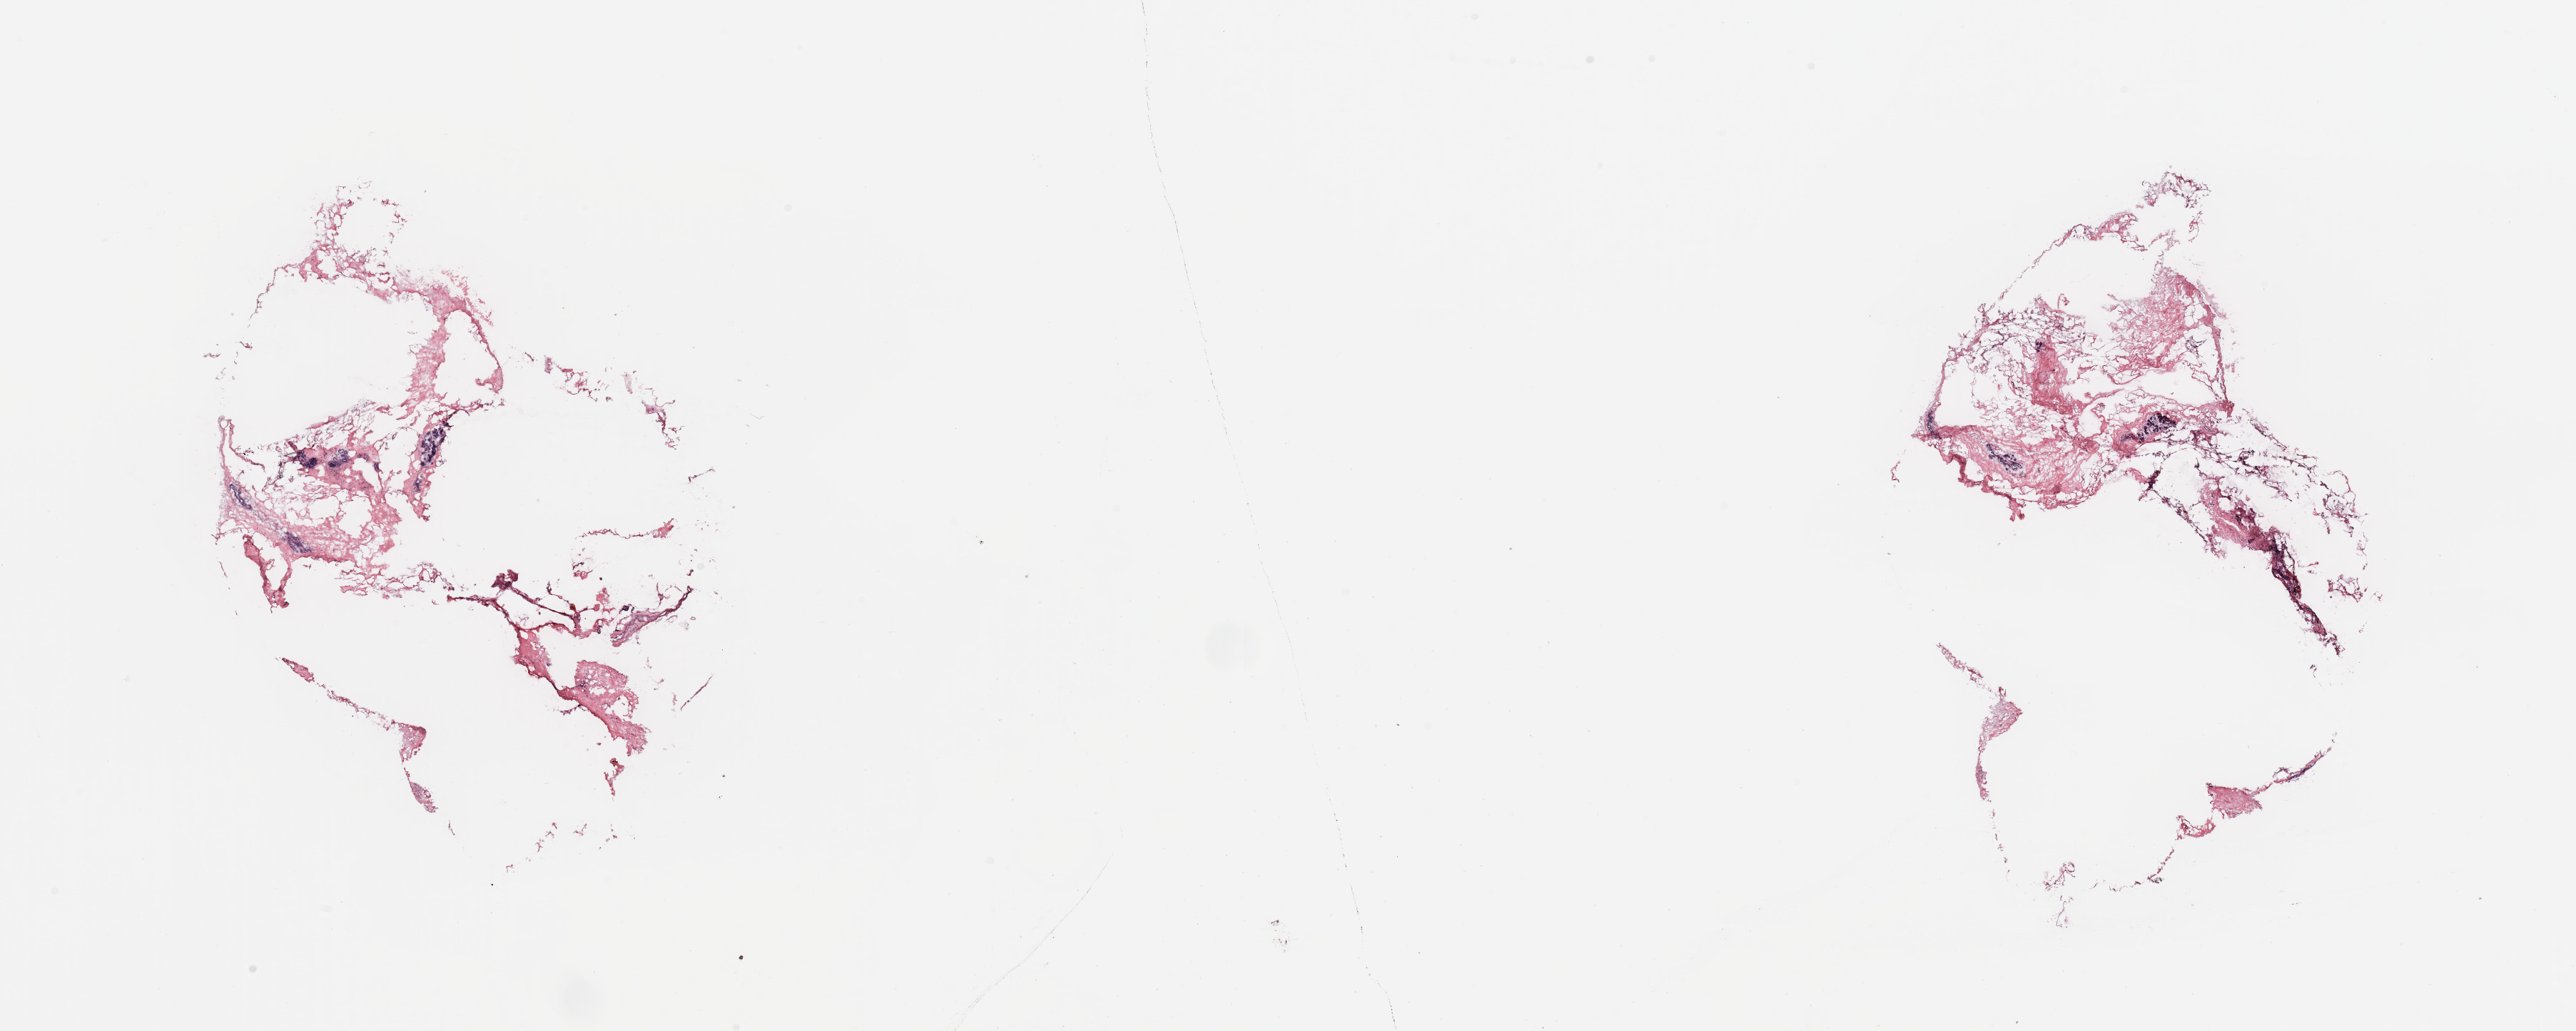
Whole-slide histology image, H&E — low-resolution overview of the scanned area, about 28.5 x 11.4 mm (acquisition: 20x scan); breast, tissue type not recorded.
Patient diagnosis (cohort enrolment): breast cancer (breast).